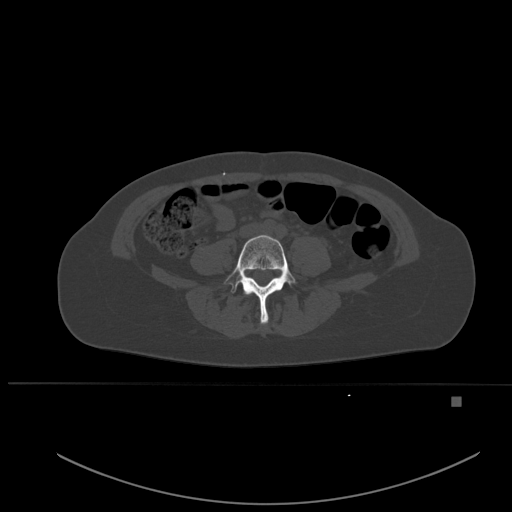
CT including the spine, one axial slice. Position 173 of 651 along the scan axis. Bone window (W 1800 / L 400 HU). 1.5 mm slice thickness. 512 × 512 image matrix, field of view 443 × 443 mm. Female patient, age 49 years. From the clinical record (not read from this slice): primary cancer: breast.
Outlined on this slice (semi-automatic segmentation, software-assisted and operator-edited):
- L4 vertebra: bounding box [x1, y1, x2, y2] px = [224, 235, 297, 324]